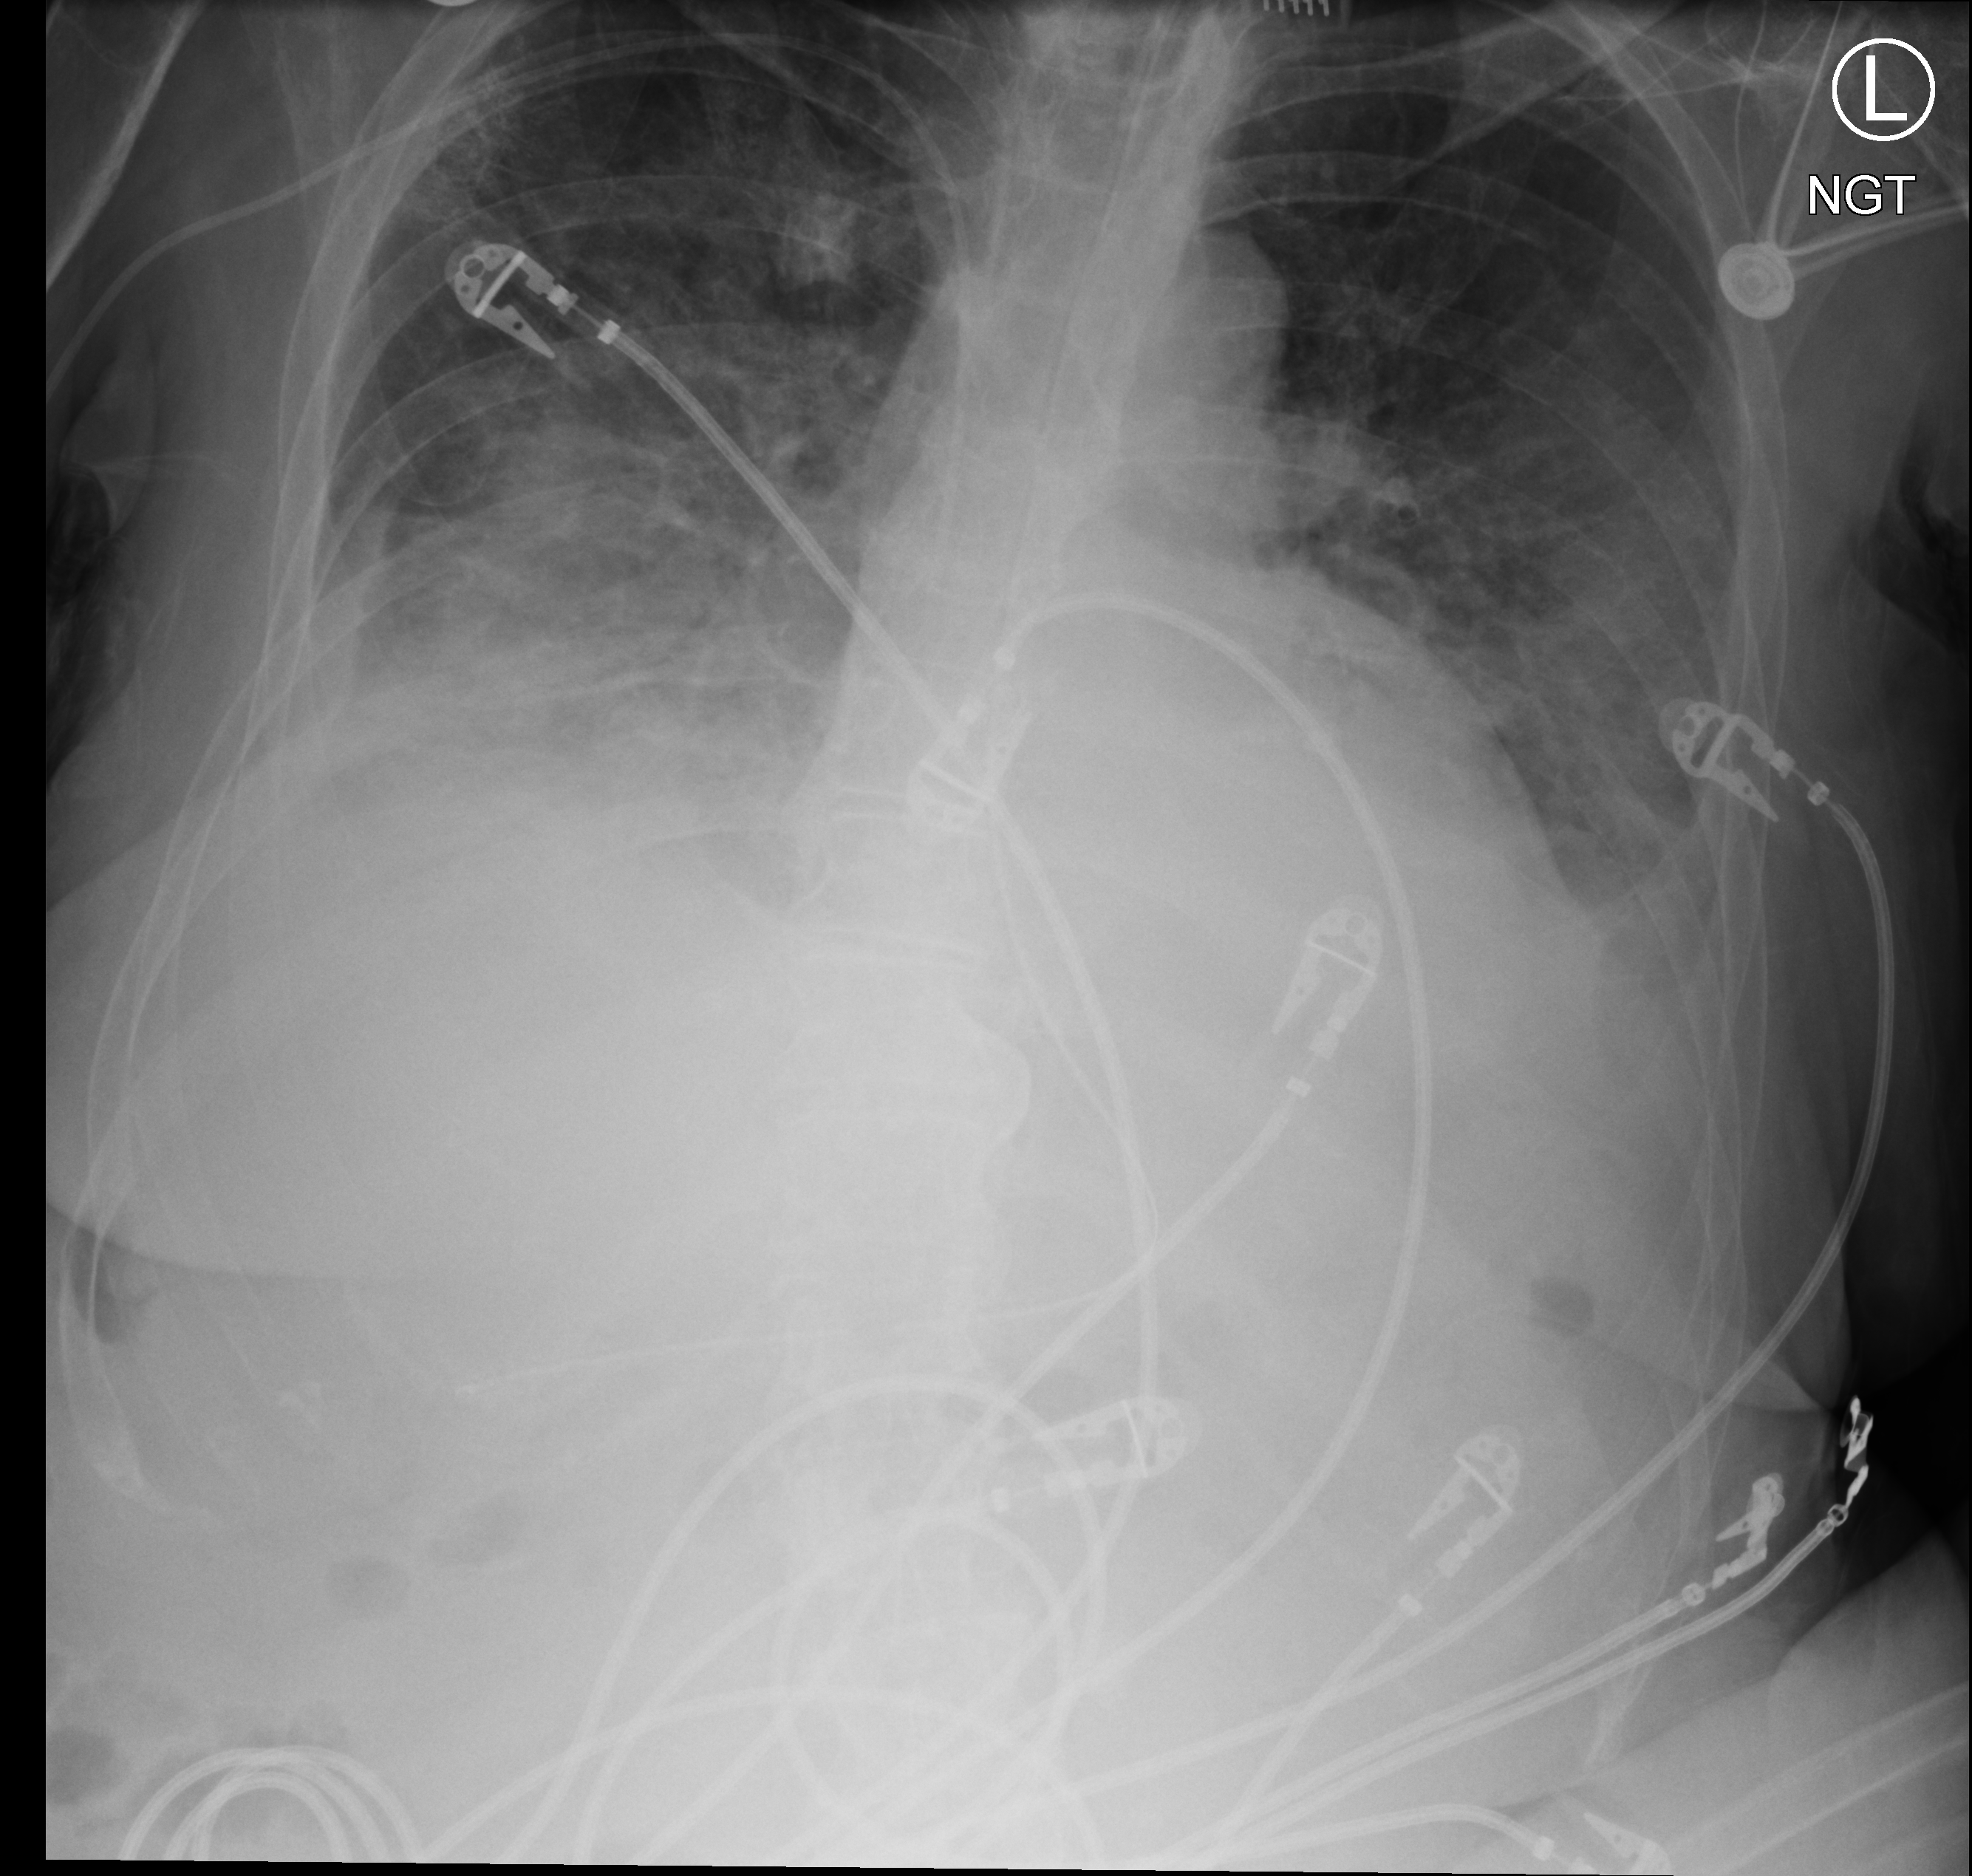
Bedside chest radiograph (computed radiography); anteroposterior (AP) projection. Female patient hospitalised with COVID-19, age 60–74 years.
From the hospital-stay record, not from the radiograph (when in the stay this image was taken is not recorded):
- length of hospital stay: 10 days
- admitted to intensive care during this hospital stay: yes